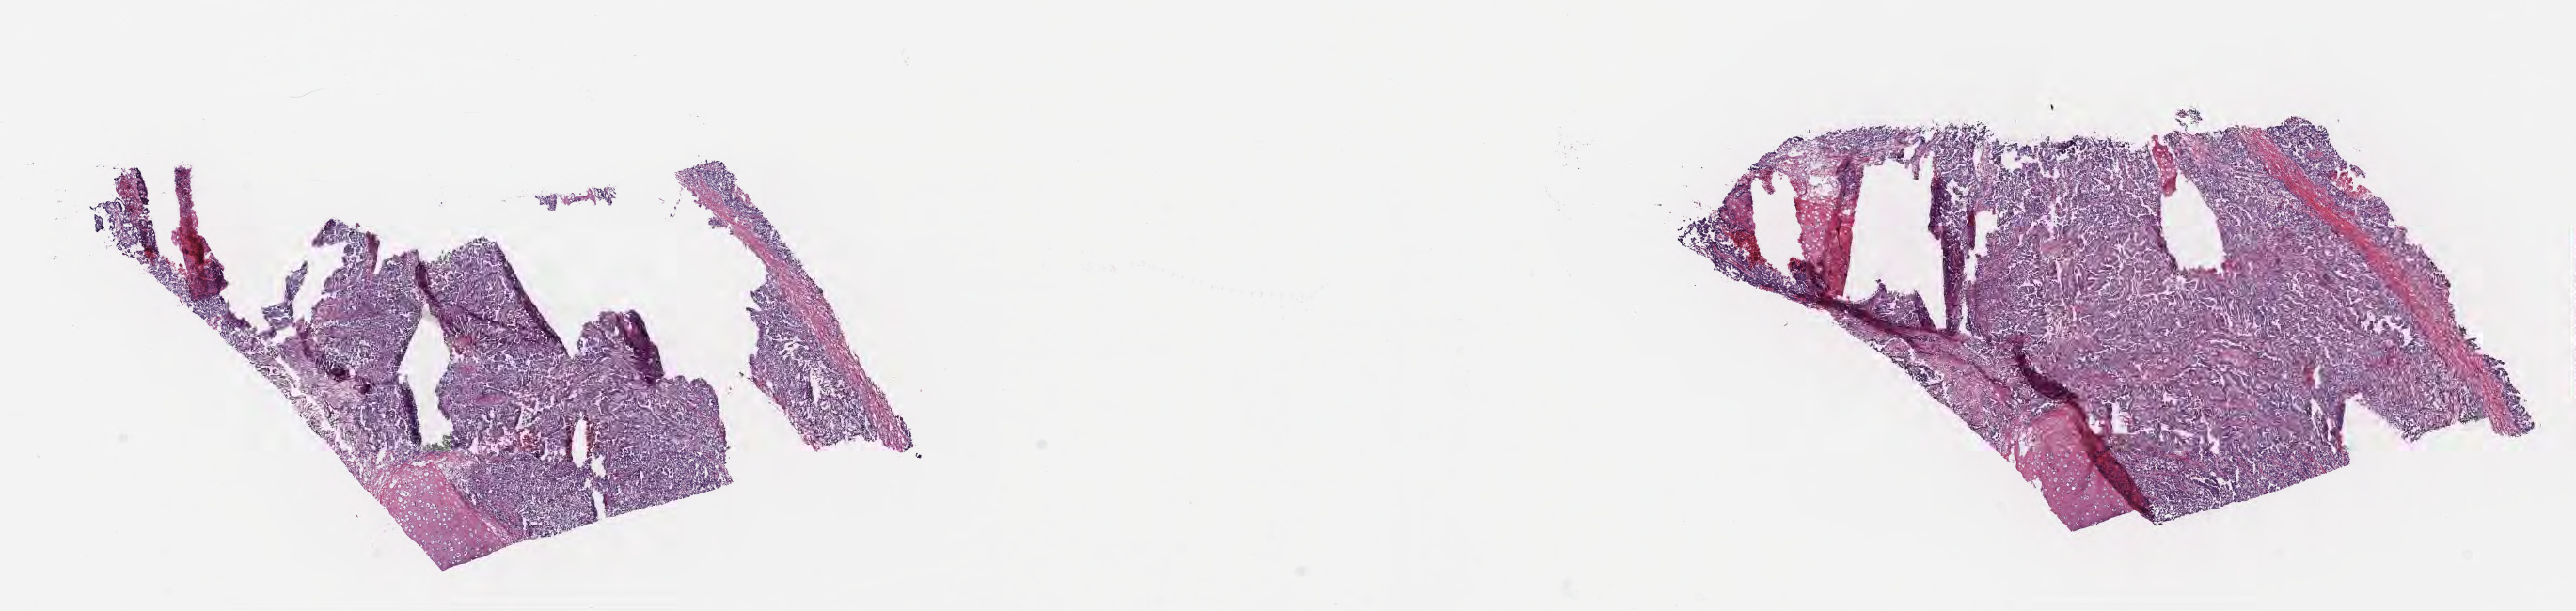
Hematoxylin and eosin (H&E) whole-slide image — whole scanned area (about 22.1 x 5.3 mm) shown as a low-resolution overview. Cryosection. Primary tumor. Site: lower lobe of right lung. Patient male; age 74 years. Pathologist review of this section (percent, as recorded): tumor cells 90%, tumor nuclei 65%, stromal cells 10%, necrosis 0%, normal cells 0%. Infiltration values recorded for this section: lymphocyte infiltration 0%, monocyte infiltration 0%, neutrophil infiltration 0%.
Histologic diagnosis: Adenocarcinoma, NOS. AJCC pathologic stage: Stage IIB.